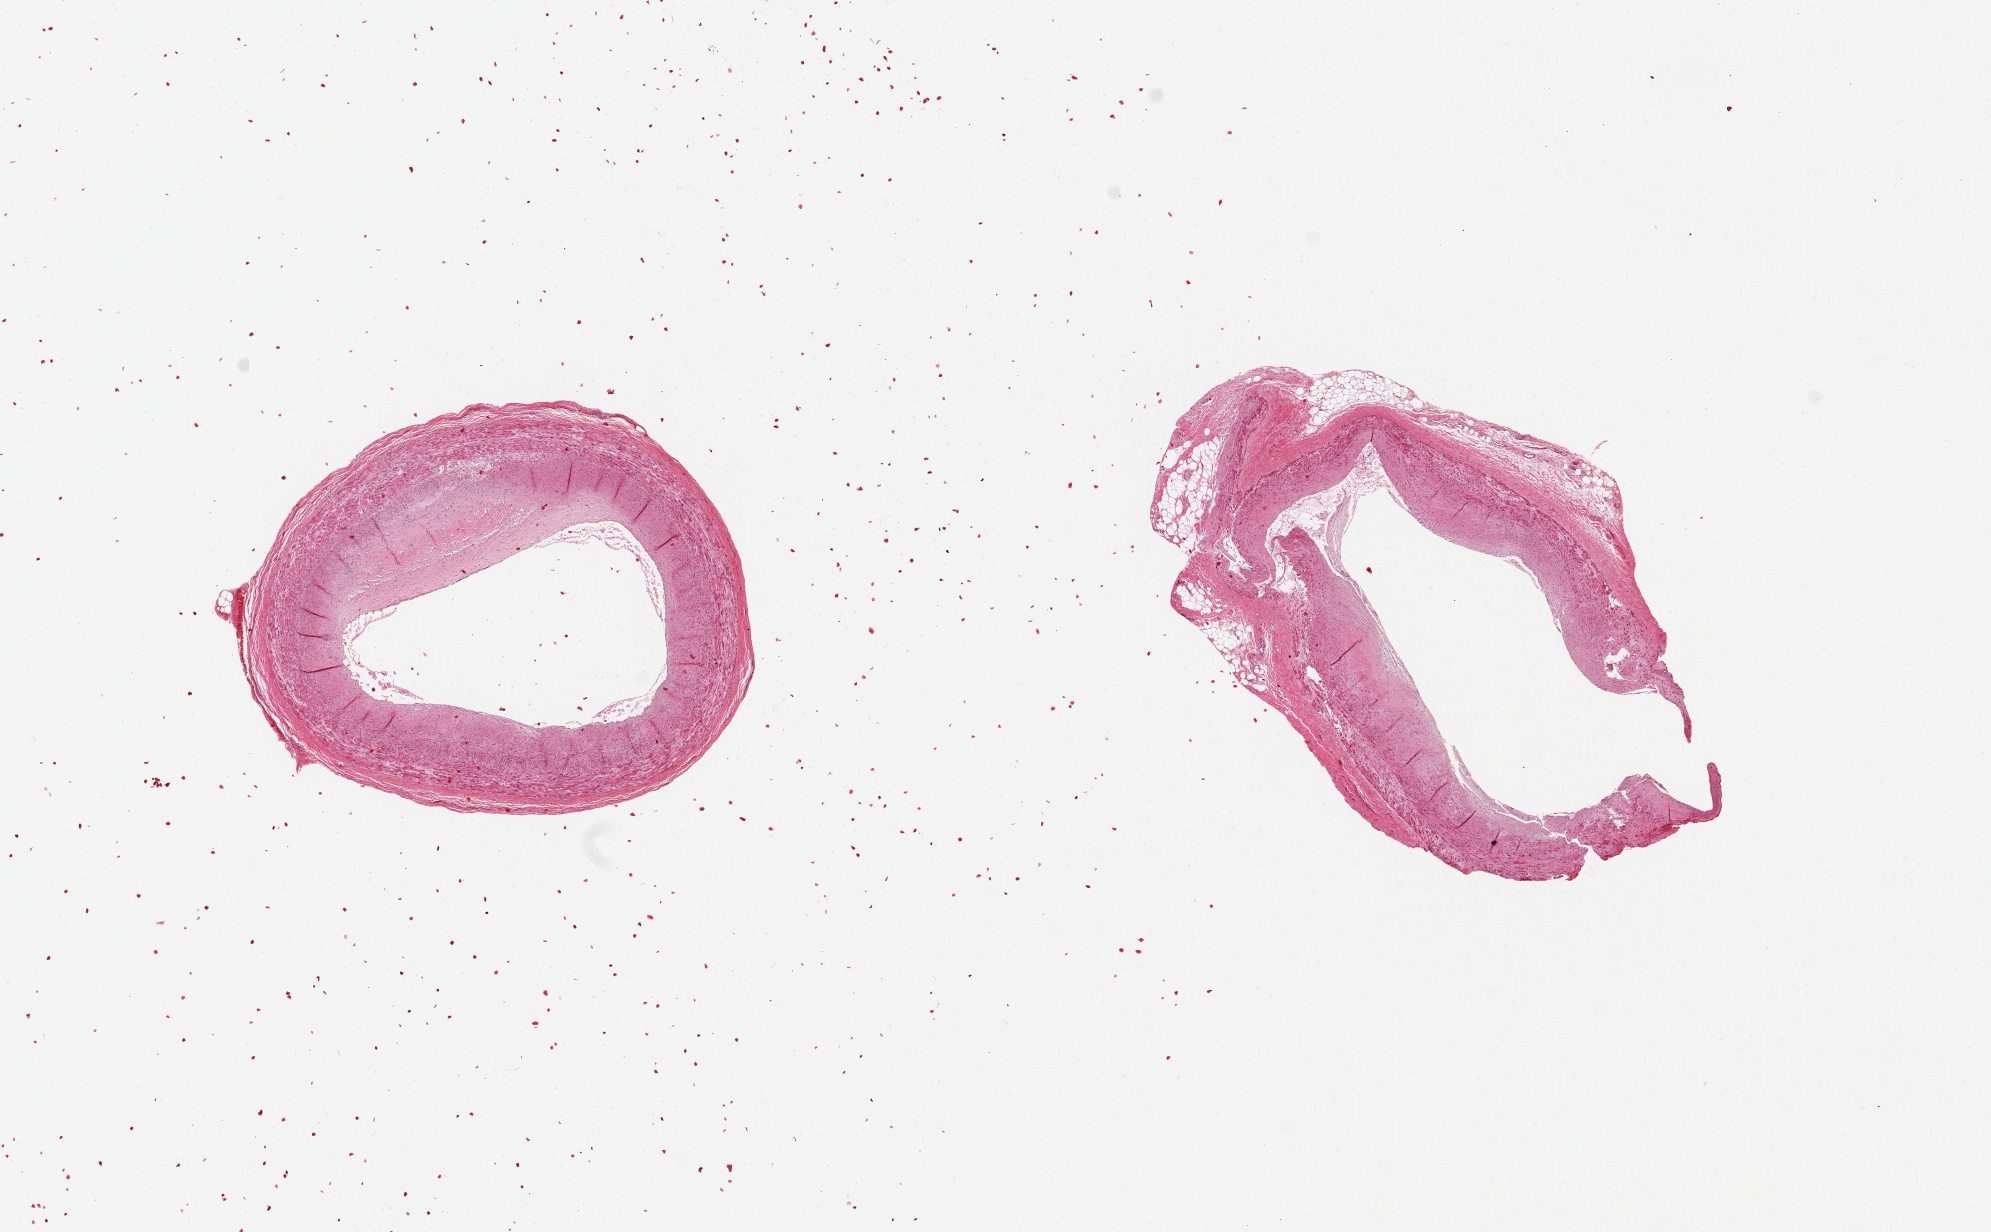
Haematoxylin and eosin whole-slide image, brightfield — shown as a low-resolution overview of the whole scanned area (about 15.8 x 9.7 mm, from a 20x scan).
Specimen: PAXgene-fixed, paraffin-embedded tissue; target tissue: coronary artery; tissue donor sample.